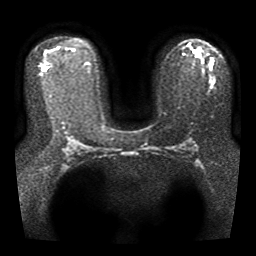
Breast MRI, one axial slice; position 23 of 41 along the scan axis; diffusion-weighted series; image 2 of 4 stored at this slice position (different b-values; order by instance number); 1.5 T; 256 × 256 image matrix, field of view 330 × 330 mm. Female patient.
Structures marked on this image (outlined manually by an expert reader):
- tumour on diffusion-weighted imaging: bounding box [x1, y1, x2, y2] px = [192, 50, 201, 57]